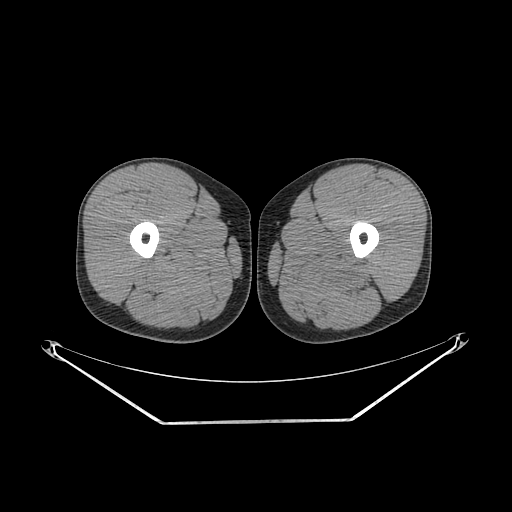
CT of an extremity soft-tissue mass (from a PET/CT study), one axial slice; position 239 of 267 along the scan axis; soft-tissue window (W 400 / L 40 HU); 3.75 mm slice thickness; 512 × 512 image matrix, field of view 500 × 500 mm. Male patient. From the clinical record (not read from this slice): histological type: extraskeletal osteosarcoma; grade: high; site of the primary tumour: left adductur.
Annotated regions visible in this slice (expert contour drawn on MRI and transferred to this co-registered scan by the dataset authors):
- gross tumour volume (mass): bounding box <281,247,380,298> (left, top, right, bottom; pixels)